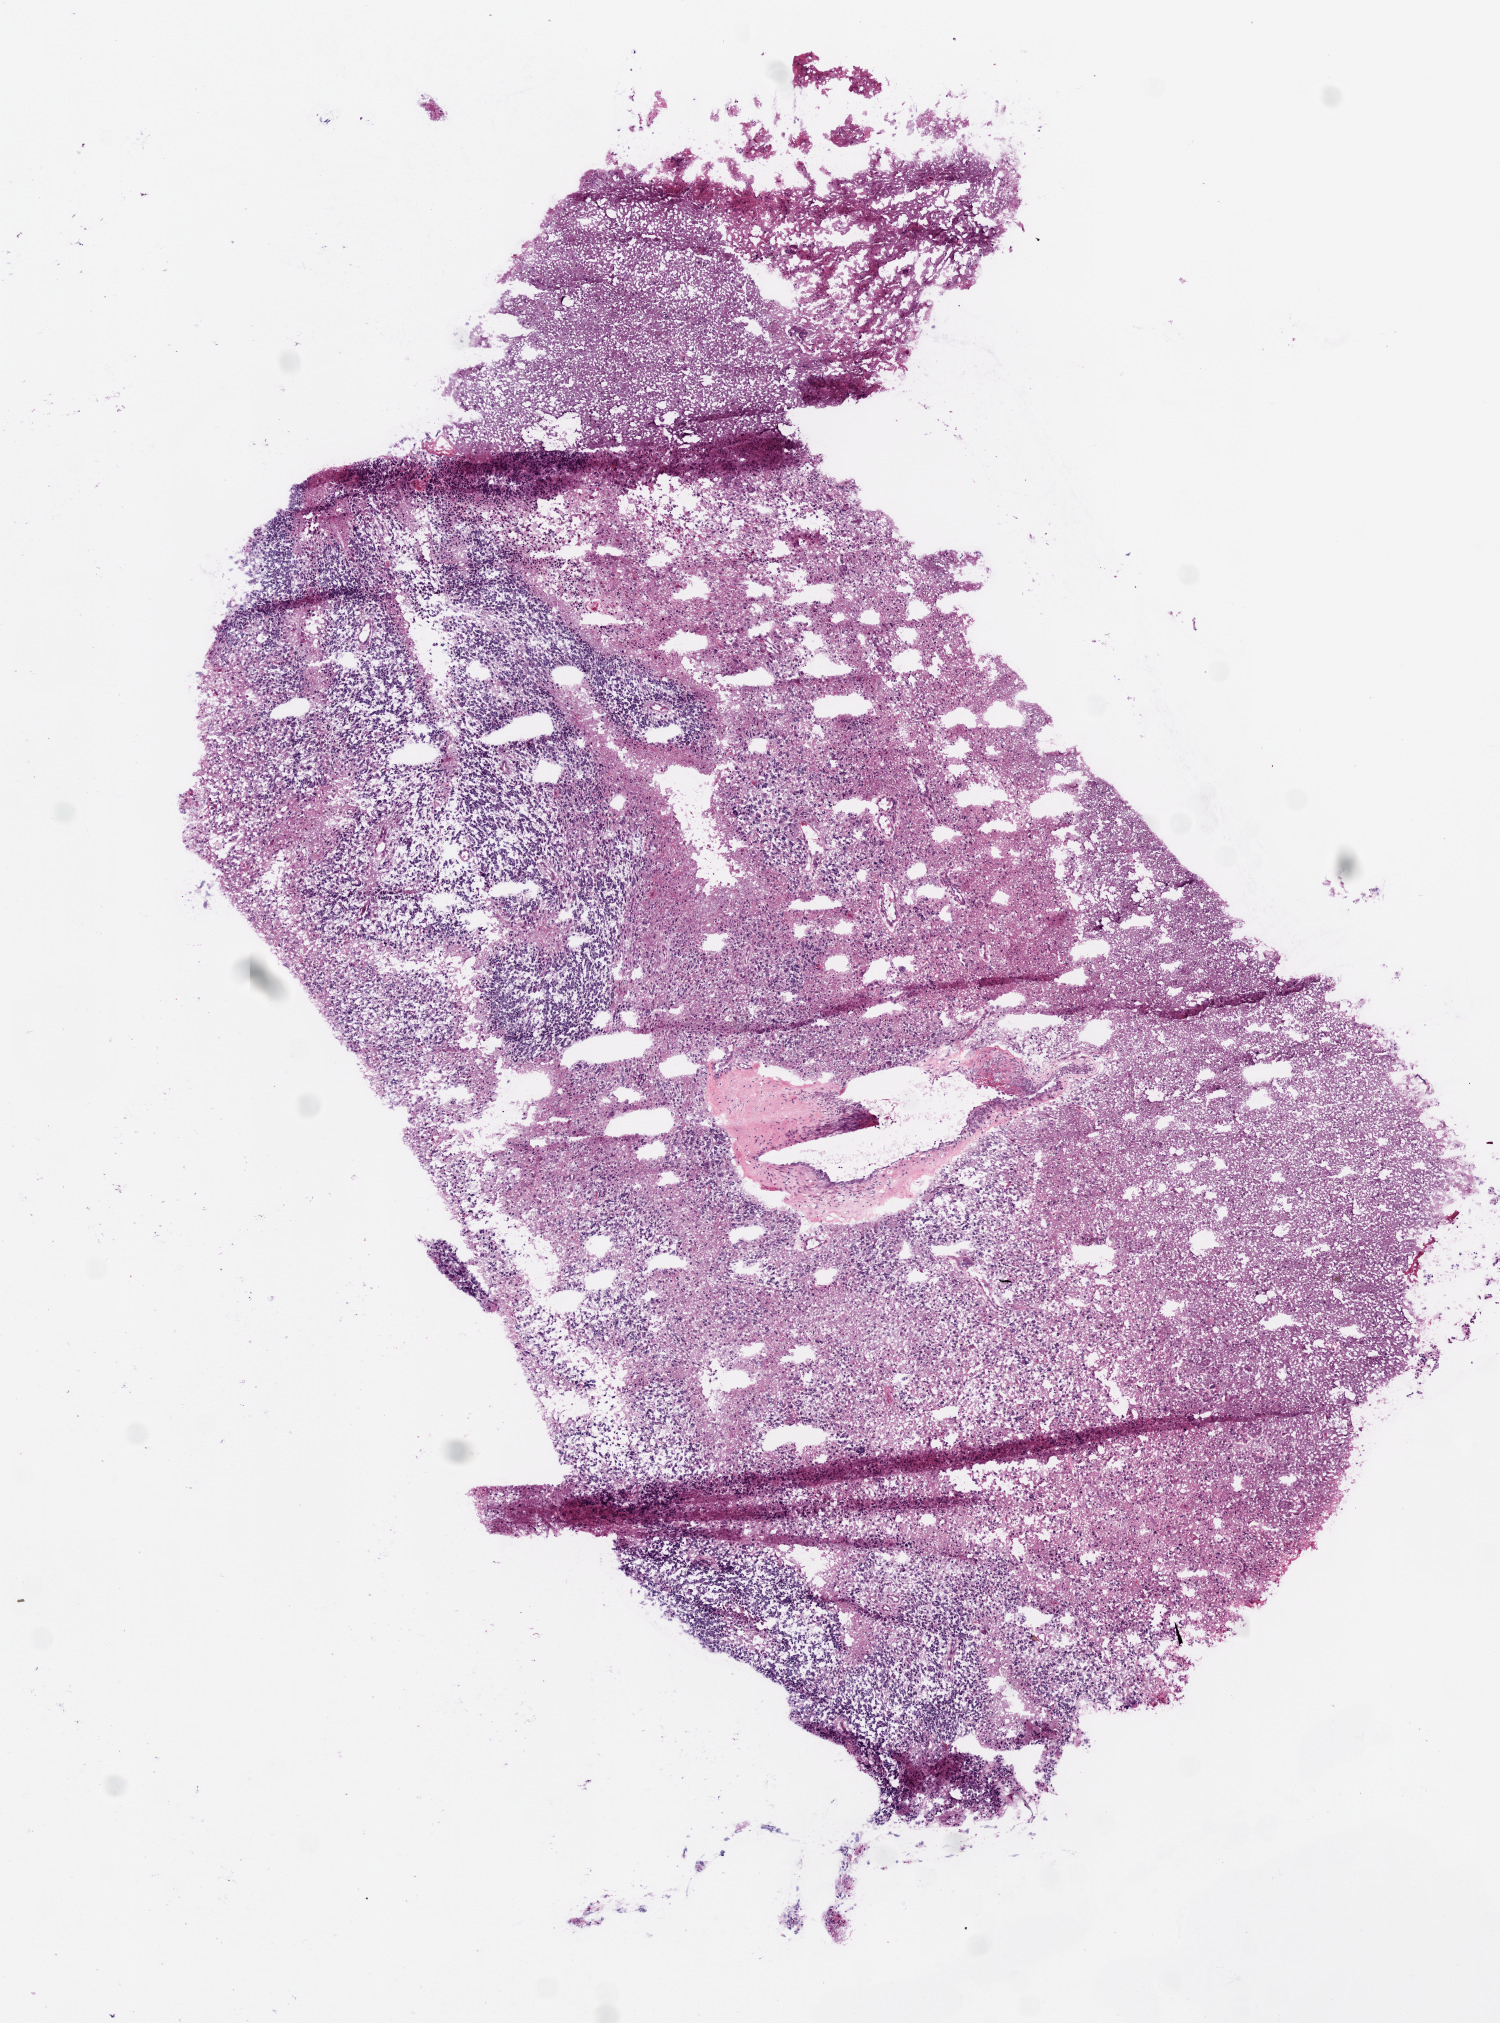
Whole-slide histology image, H&E, a low-resolution overview of the entire scanned area, about 6.0 x 8.1 mm (from a 20x scan); frozen section from the bottom of the tissue portion; primary tumour sample from the brain. Male, age 82 years at initial diagnosis. Pathologist review of this section (percent, as recorded): tumour cells 85%, tumour nuclei 80%, normal cells 0%, stromal cells 0%, necrosis 15%.
Diagnosis: Glioblastoma.